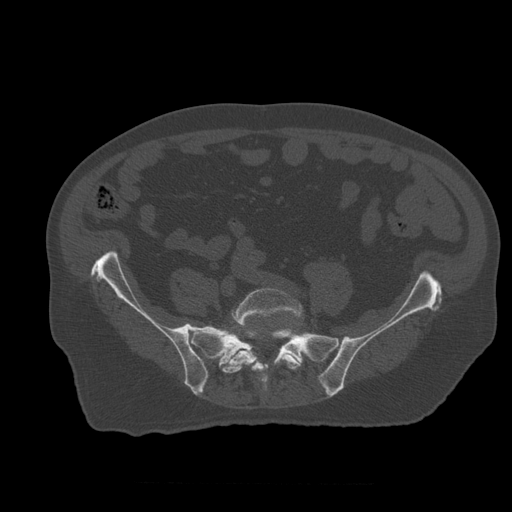
CT including the spine, one axial slice; position 131 of 399 along the scan axis; reconstruction kernel STANDARD; 120 kVp; bone window (W 1800 / L 400 HU); 1.25 mm slice thickness; 512 × 512 image matrix, field of view 407 × 407 mm. Patient age 73 years. From the clinical record (not read from this slice): primary cancer: prostate; vertebrae with lytic lesions (as recorded): L2.
Structures marked on this image (semi-automatic segmentation, software-assisted and operator-edited):
- L5 vertebra: bounding box <222,288,303,387> (left, top, right, bottom; pixels)